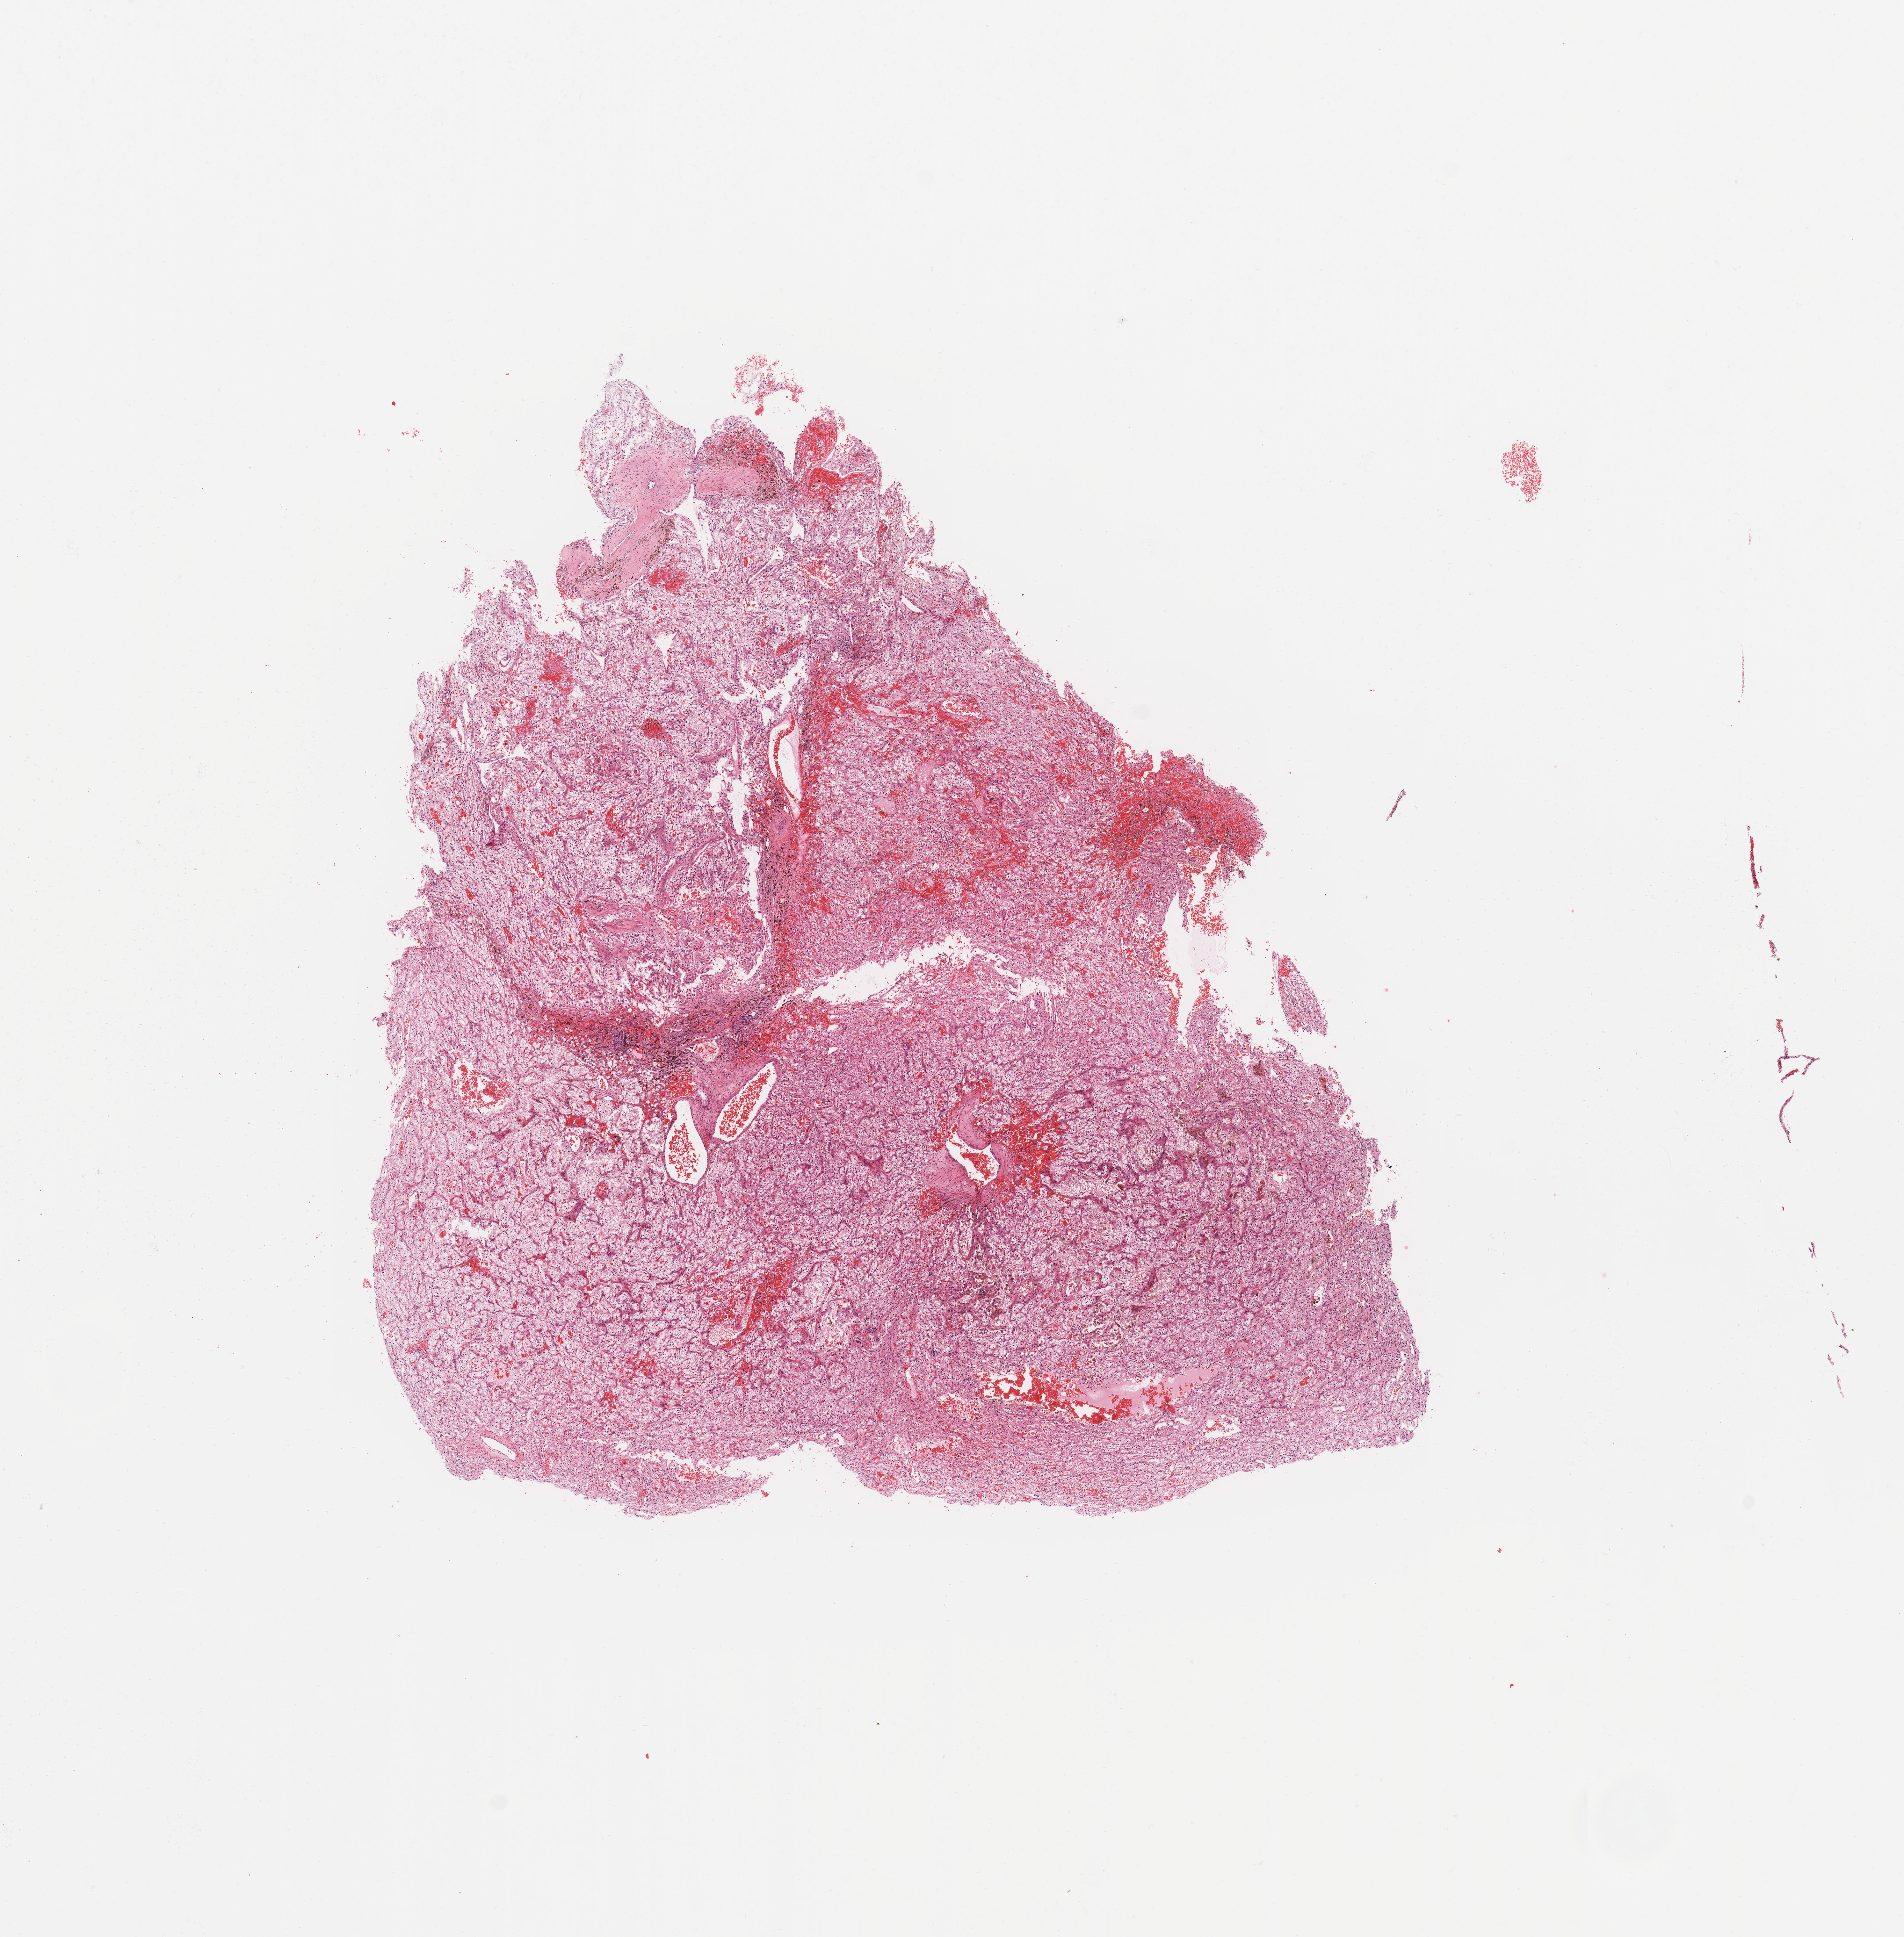
Hematoxylin and eosin (H&E) stained whole-slide image, whole scanned area (about 11.8 x 12.0 mm, slide scanned at 20x) shown as a low-resolution overview; tumour tissue sample, sampled site: kidney. 76-year-old male patient. Histologic grade: G2 (moderately differentiated). Slide review estimates, as recorded: tumour nuclei 90%, necrosis 0%.
Primary tumour site (as recorded): upper pole. AJCC pathologic stage: I. Diagnosis: Renal cell carcinoma, NOS.